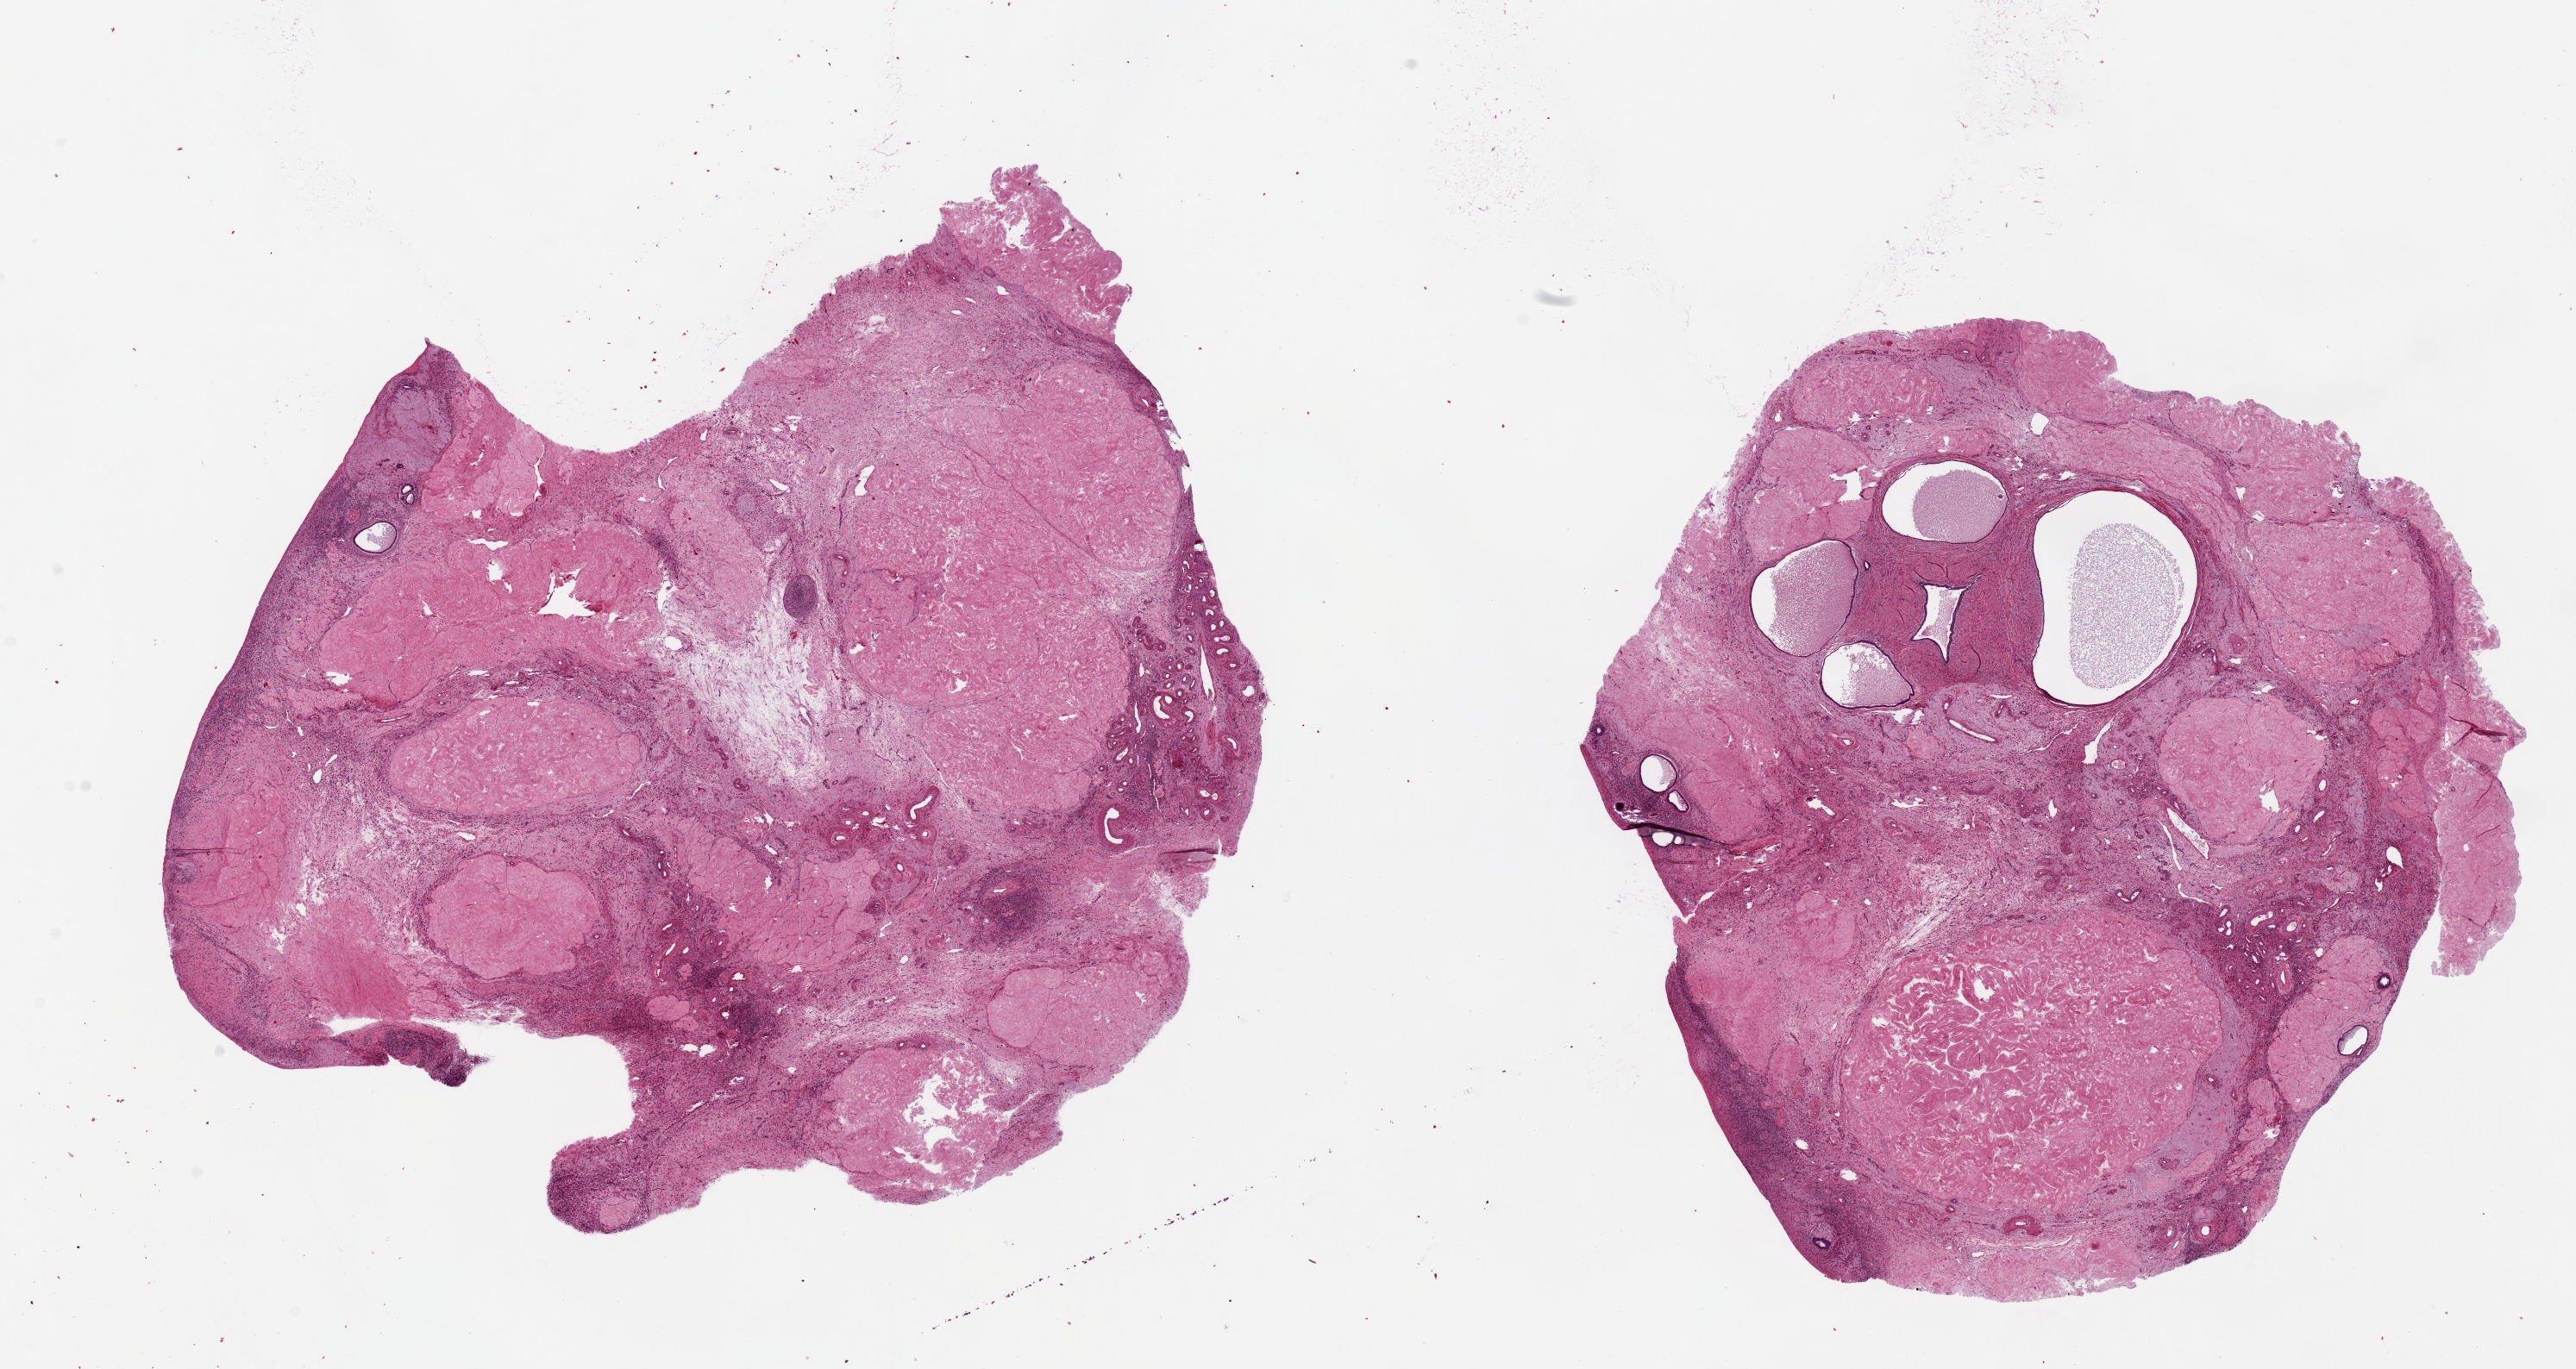
Digitized H&E-stained section, shown as a low-resolution overview of the whole scanned area (about 23.6 x 12.6 mm, slide scanned at 20x). PAXgene-fixed, paraffin-embedded tissue. Section of ovary (target tissue). Tissue donor sample.
* reviewer comment on this tissue sample: 2 pieces, 10.5x10 & 9x8mm; small (0.5--2mm) serous cystadenomas in one aliquot